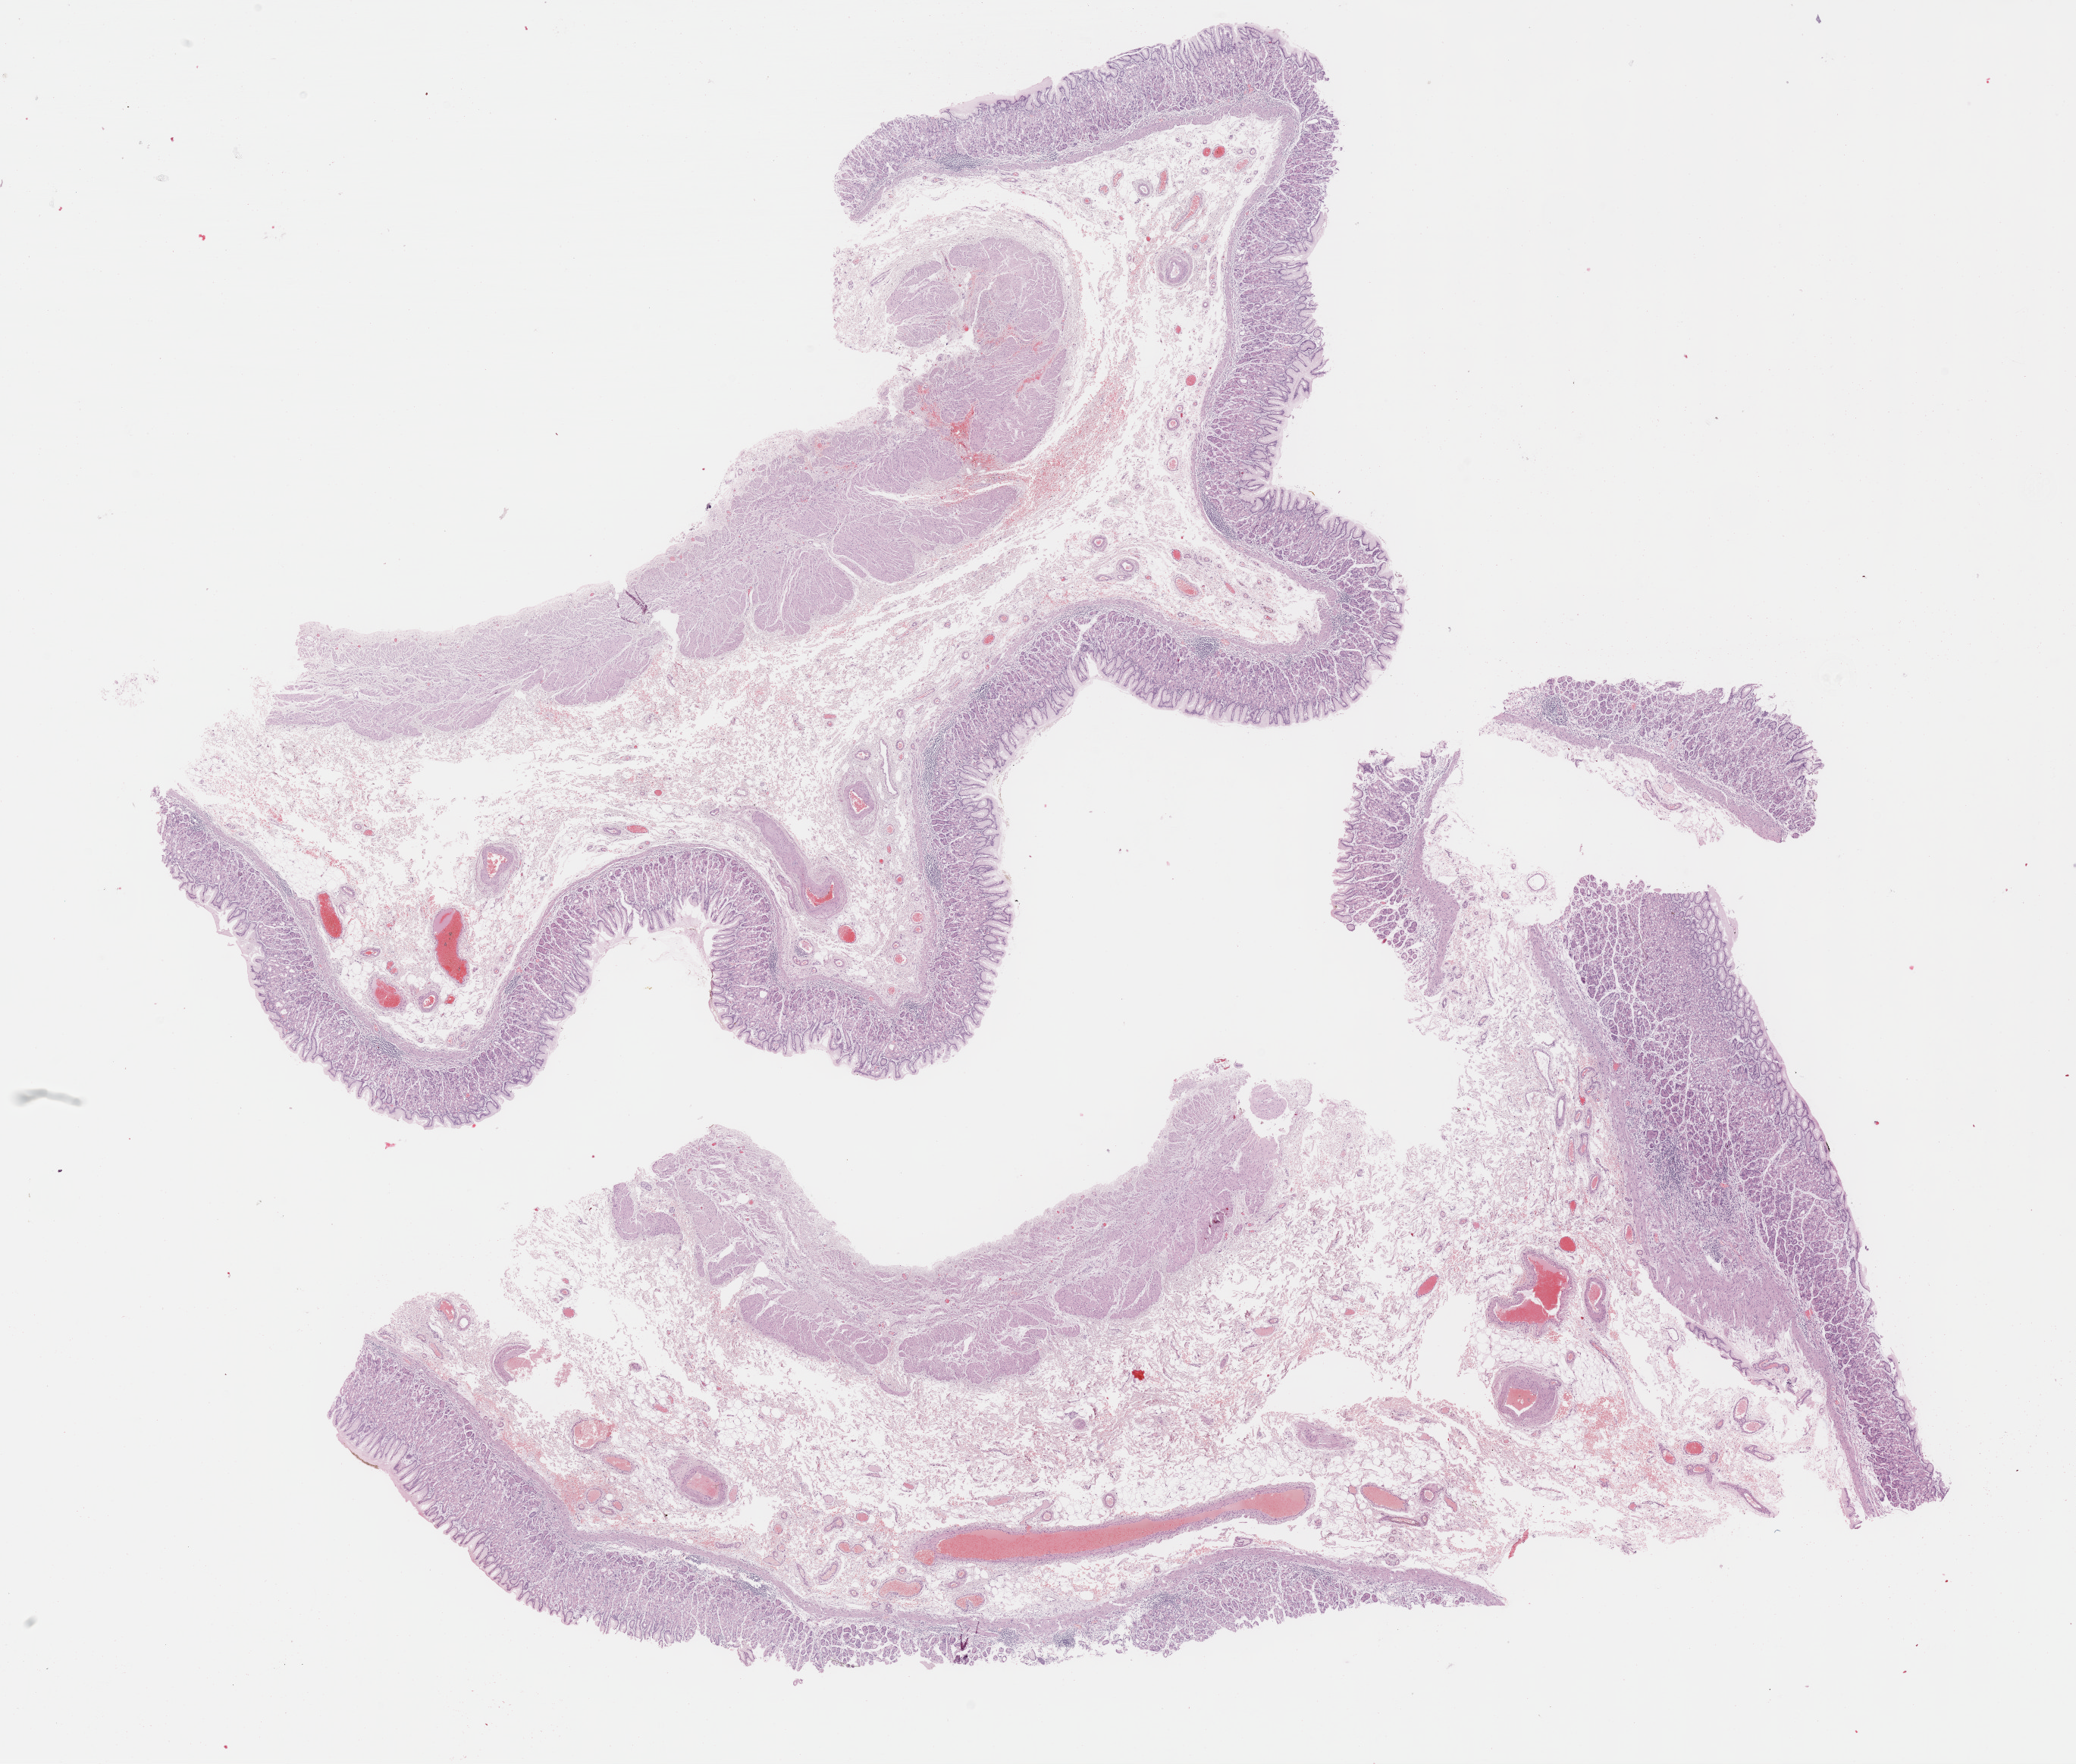
Digitized Hematoxylin and eosin (H&E) stained tissue section (whole slide) — a low-resolution overview of the entire scanned area, about 22.1 x 18.8 mm (slide scanned at 40x), FFPE section, sample: primary tumour, stomach. Patient: female, age at initial diagnosis 72 years. Histologic grade: G3 (poorly differentiated).
• diagnosis: Tubular adenocarcinoma (gastric antrum)
• TNM: T3 N2 M0
• AJCC pathologic stage: IIIA (7th edition)